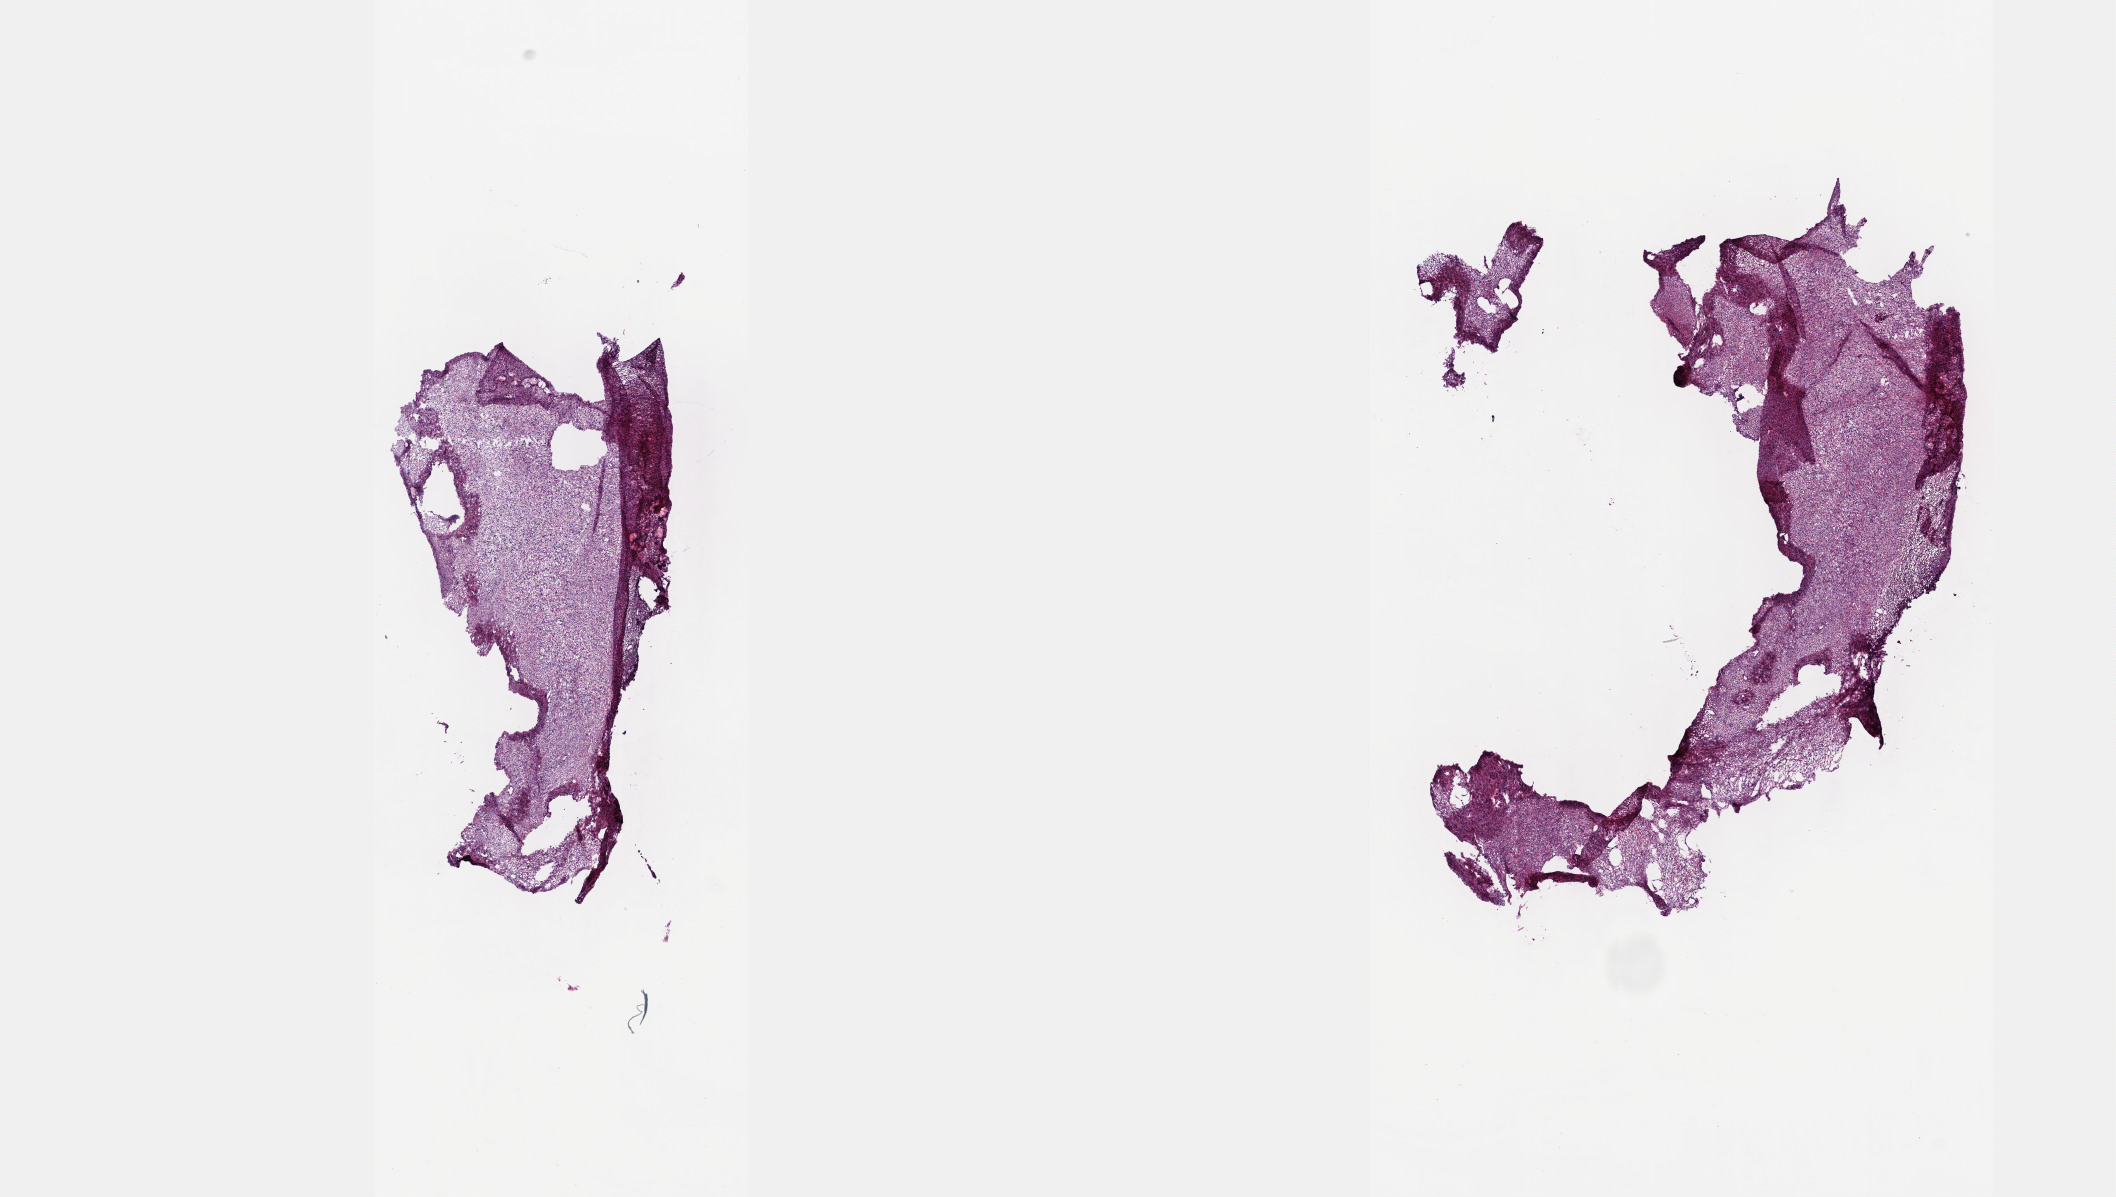
Whole-slide histology image, H&E-stained, whole scanned area (about 17.1 x 9.7 mm, slide scanned at 40x) shown as a low-resolution overview; frozen section; sample: primary tumour, connective, subcutaneous and other soft tissues. Female, age 68 years at initial diagnosis. Composition of this section per pathologist review: tumour cells 95%, tumour nuclei 95%, normal cells 0%, stromal cells 5%, necrosis 0%. Inflammatory infiltration, as recorded: lymphocyte infiltration 0%, monocyte infiltration 0%, neutrophil infiltration 0%.
Diagnosis: Malignant peripheral nerve sheath tumor.